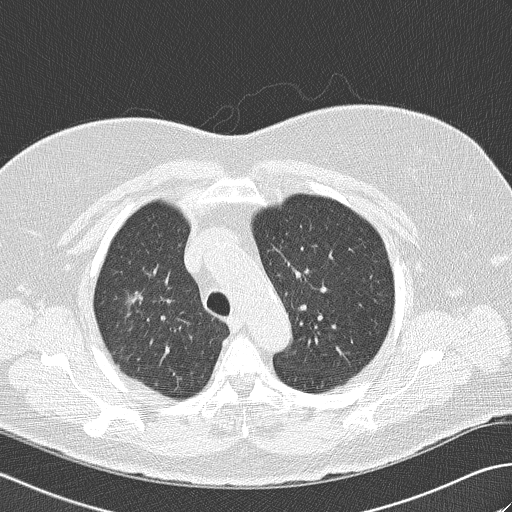
Axial slice from a low-dose chest CT screening exam. Second annual screen. Lung window (W 1500 / L -600 HU). 2 mm slice thickness. Slice 117 of 148 in the series. Female participant, aged 74 years at enrolment.
Lesion marked by an expert reader, bounding box <104,280,163,331> (left, top, right, bottom; pixels). The screening reader recorded 4 non-calcified nodules or masses ≥4 mm on this exam (right upper lobe, right middle lobe, right middle lobe, left lower lobe); which of them this box marks is not recorded. Official screen result: positive, other.